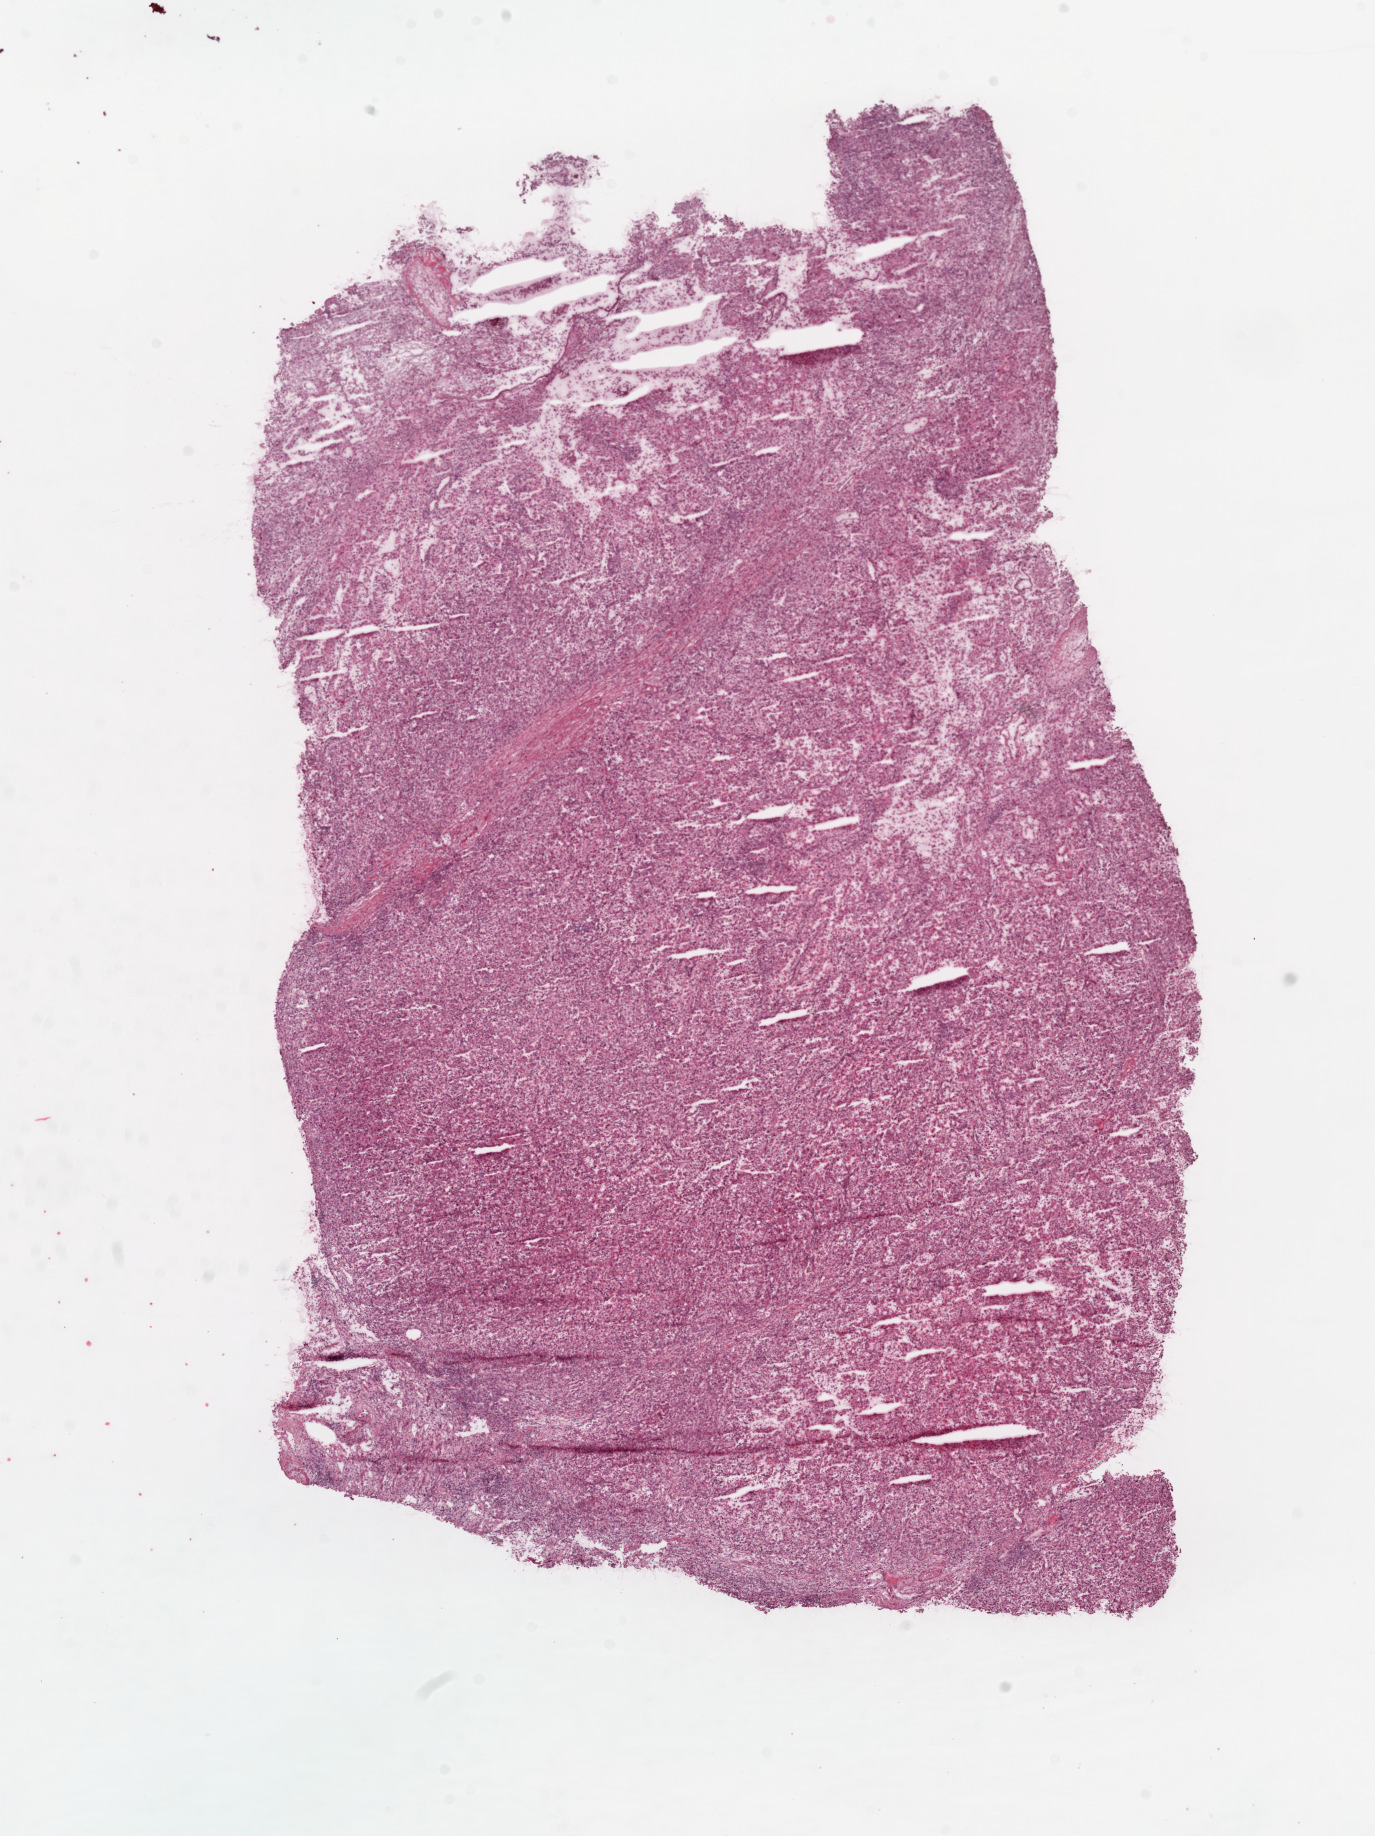
Digitized Hematoxylin and eosin (H&E) stained tissue section (whole slide), whole scanned area (about 11.0 x 14.7 mm, from a 20x scan) shown as a low-resolution overview; frozen section from the top of the tissue portion; primary tumour sample from the kidney. Male, age 74 years at initial diagnosis. Histologic grade: G4 (undifferentiated). Pathologist review of this section (percent, as recorded): tumour cells 100%, tumour nuclei 95%, normal cells 0%, stromal cells 0%, necrosis 0%.
* laterality: left
* pathologic diagnosis: Clear cell adenocarcinoma, NOS
* lymph nodes positive (case pathology): 0 of 30 examined